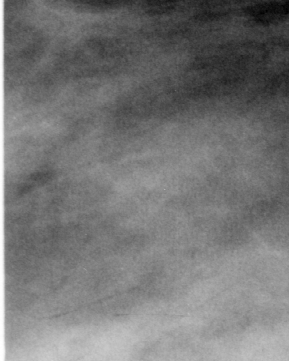
Cropped region of a digitized screen-film mammogram centred on a radiologist-marked abnormality, left breast, CC view, BI-RADS breast density category 2 (scale 1–4).
- Calcifications, morphology pleomorphic / fine linear branching, distribution regional; BI-RADS assessment category 5; subtlety rating 3 on a 1 (subtle) to 5 (obvious) scale; pathology (as recorded): malignant.